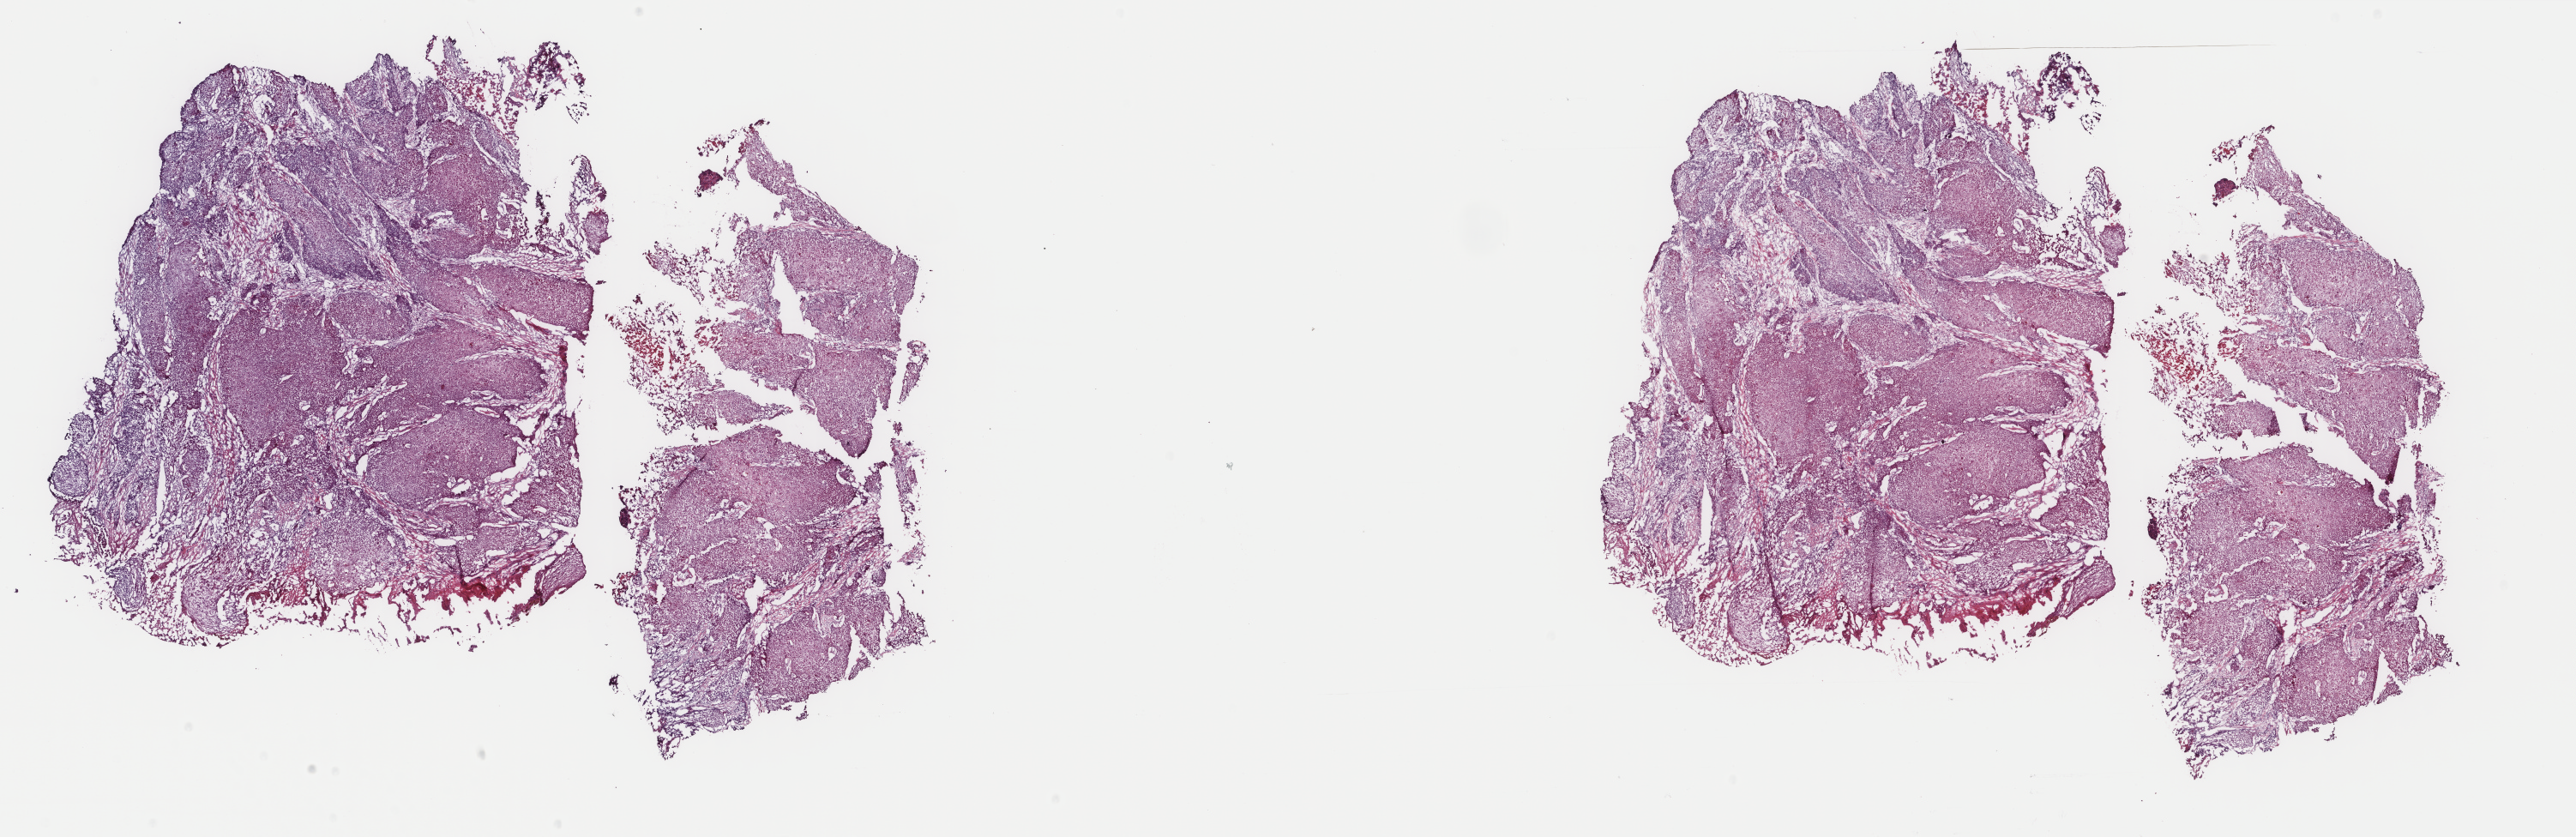
H&E-stained whole-slide image — shown as a low-resolution overview of the whole scanned area (about 23.8 x 7.7 mm); frozen section from the top of the tissue portion; esophagus, primary tumour sample. Male, age 50 years at initial diagnosis. Histologic grade: G2 (moderately differentiated). Composition of this section per pathologist review: tumour cells 85%, tumour nuclei 90%, normal cells 0%, stromal cells 15%, necrosis 0%. Inflammatory infiltration, as recorded: lymphocyte infiltration 0%, monocyte infiltration 0%, neutrophil infiltration 0%.
Pathologic diagnosis: Squamous cell carcinoma, NOS (cardia, NOS). Lymph nodes positive (case pathology): 5 of 18 examined. AJCC pathologic stage: III (6th edition).